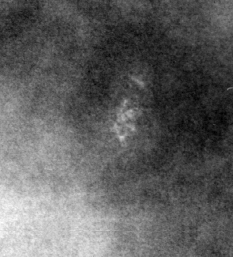
Crop from a digitized film mammogram around one marked abnormality; right breast; CC view.
Calcifications, morphology pleomorphic, distribution clustered; BI-RADS assessment category 4; pathology (as recorded): benign.